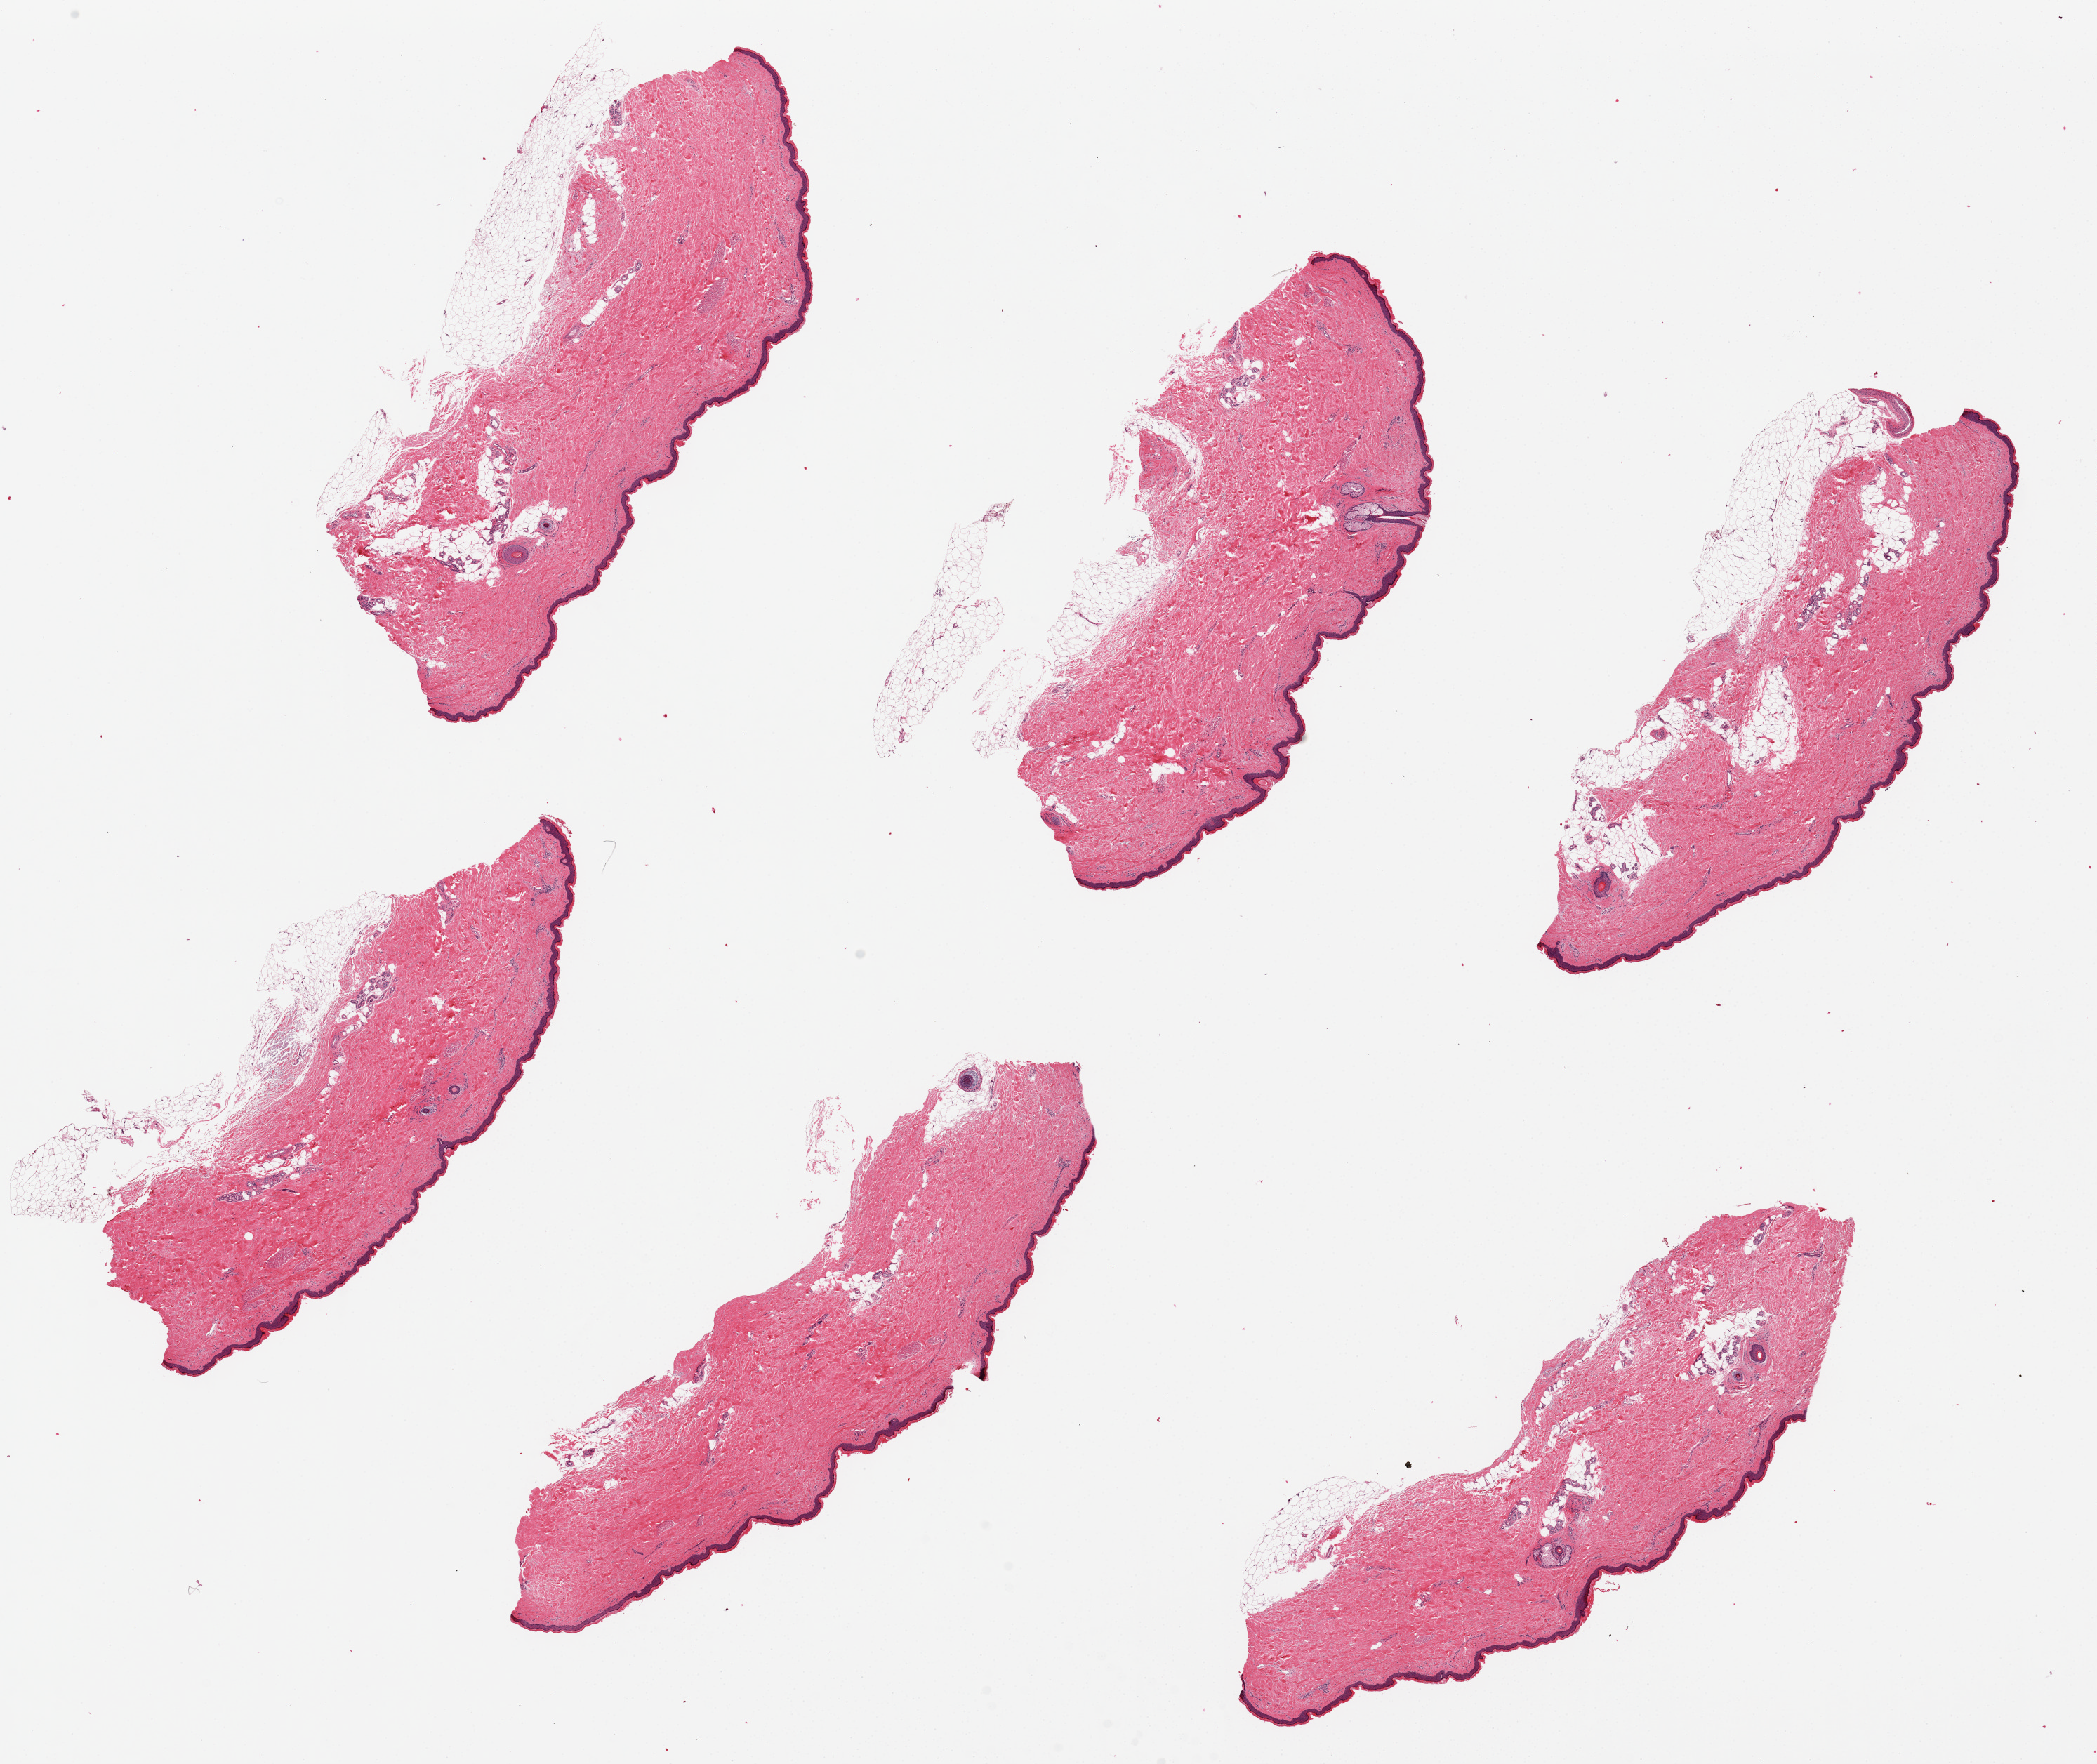
Whole-slide image, hematoxylin and eosin (H&E) stain — a low-resolution overview of the entire scanned area, about 23.6 x 19.9 mm. PAXgene-fixed, paraffin-embedded tissue. Sampled site (target tissue): skin of lower leg. Donor tissue sample.
Reviewer comment on this tissue sample: 6 pieces, some have adherent fat up to ~1mm; squamous epithelium is ~50-60microns thick.